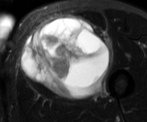
MRI of an extremity soft-tissue mass, one axial slice. Slice 35 of 52 in the series (ordered by position). T2-weighted fat-saturated. MR volume resampled by the dataset authors to the PET/CT grid (not the native acquisition matrix). 3.27 mm slice thickness. 147 × 122 image matrix. Male patient. Case-level facts recorded for this patient, not image findings: histological type: pleiomorphic liposarcoma; grade: high; site of the primary tumour: left thigh.
Structures marked on this image (expert contour drawn on MRI and transferred to this co-registered scan by the dataset authors):
- gross tumour volume including surrounding oedema: bounding box <23,16,113,97> (left, top, right, bottom; pixels)
- gross tumour volume (mass): <23,16,110,97>